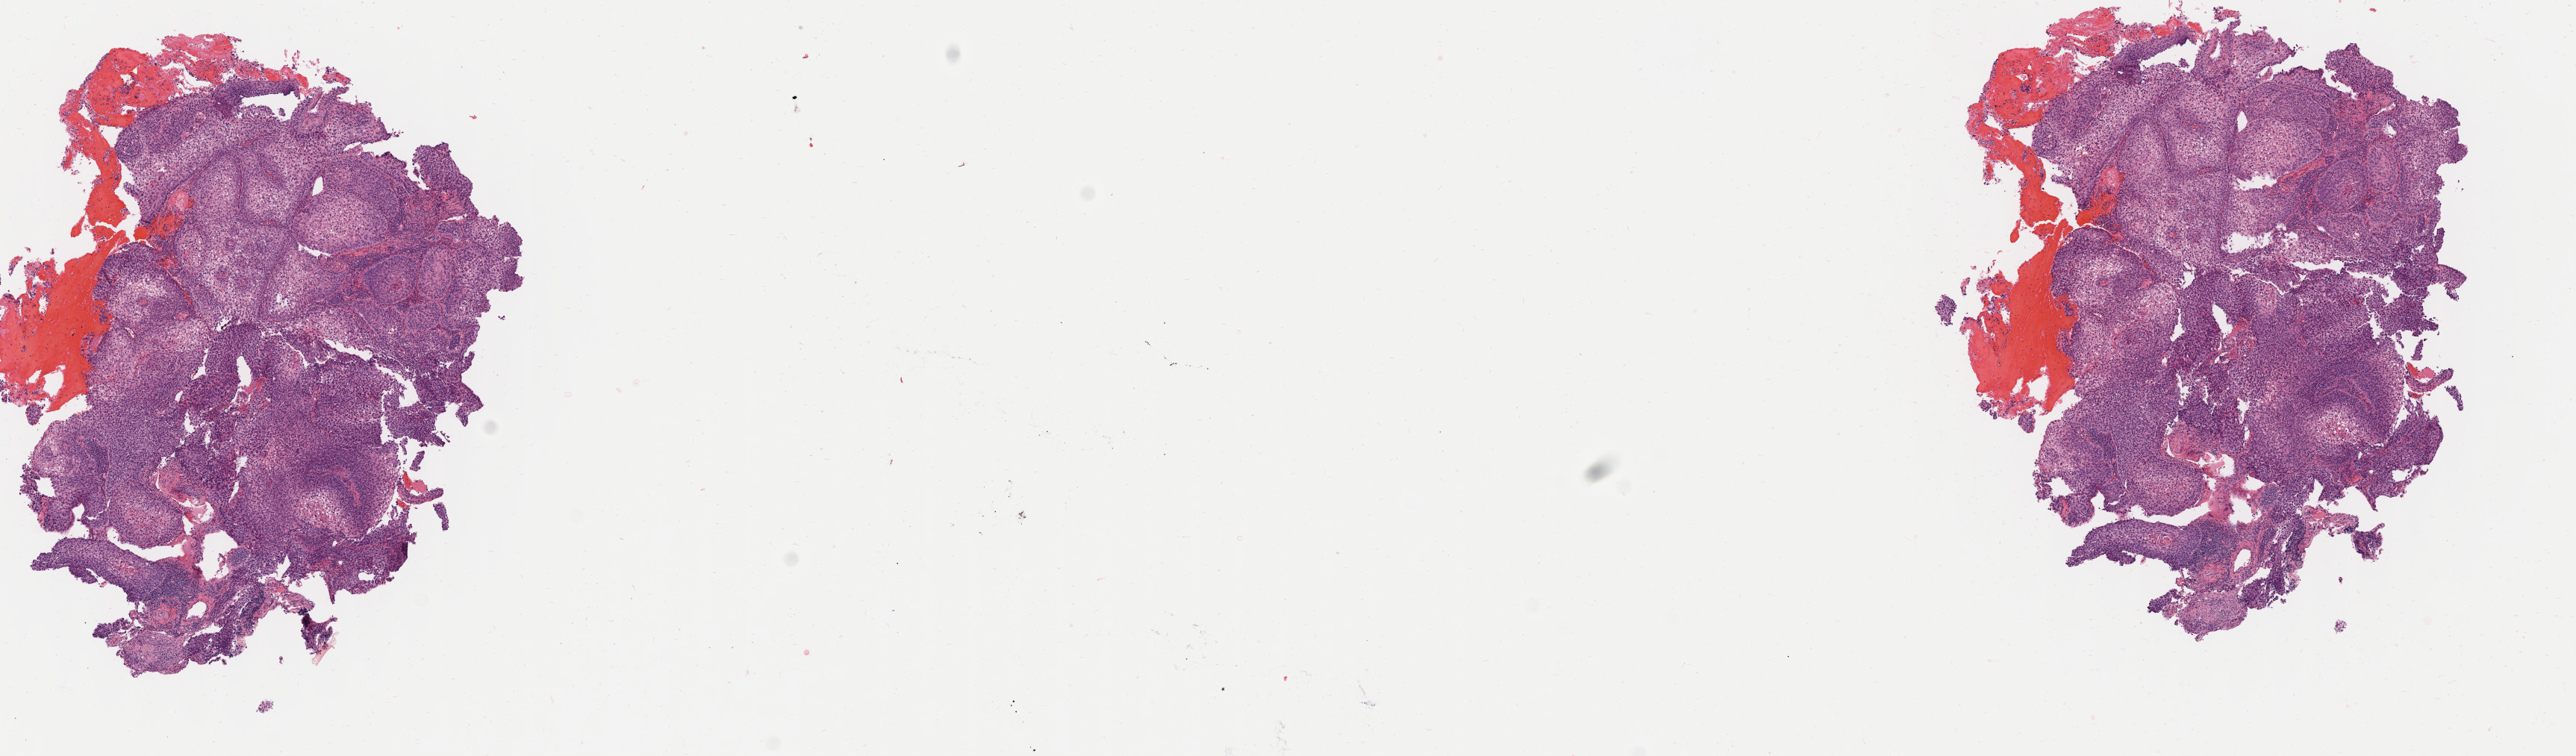
H&E whole-slide image, shown as a low-resolution overview of the whole scanned area (about 13.7 x 4.0 mm), tumor tissue, anatomic site: cervix. Patient: female, aged 30.
* histologic diagnosis: Squamous cell carcinoma, keratinizing, NOS